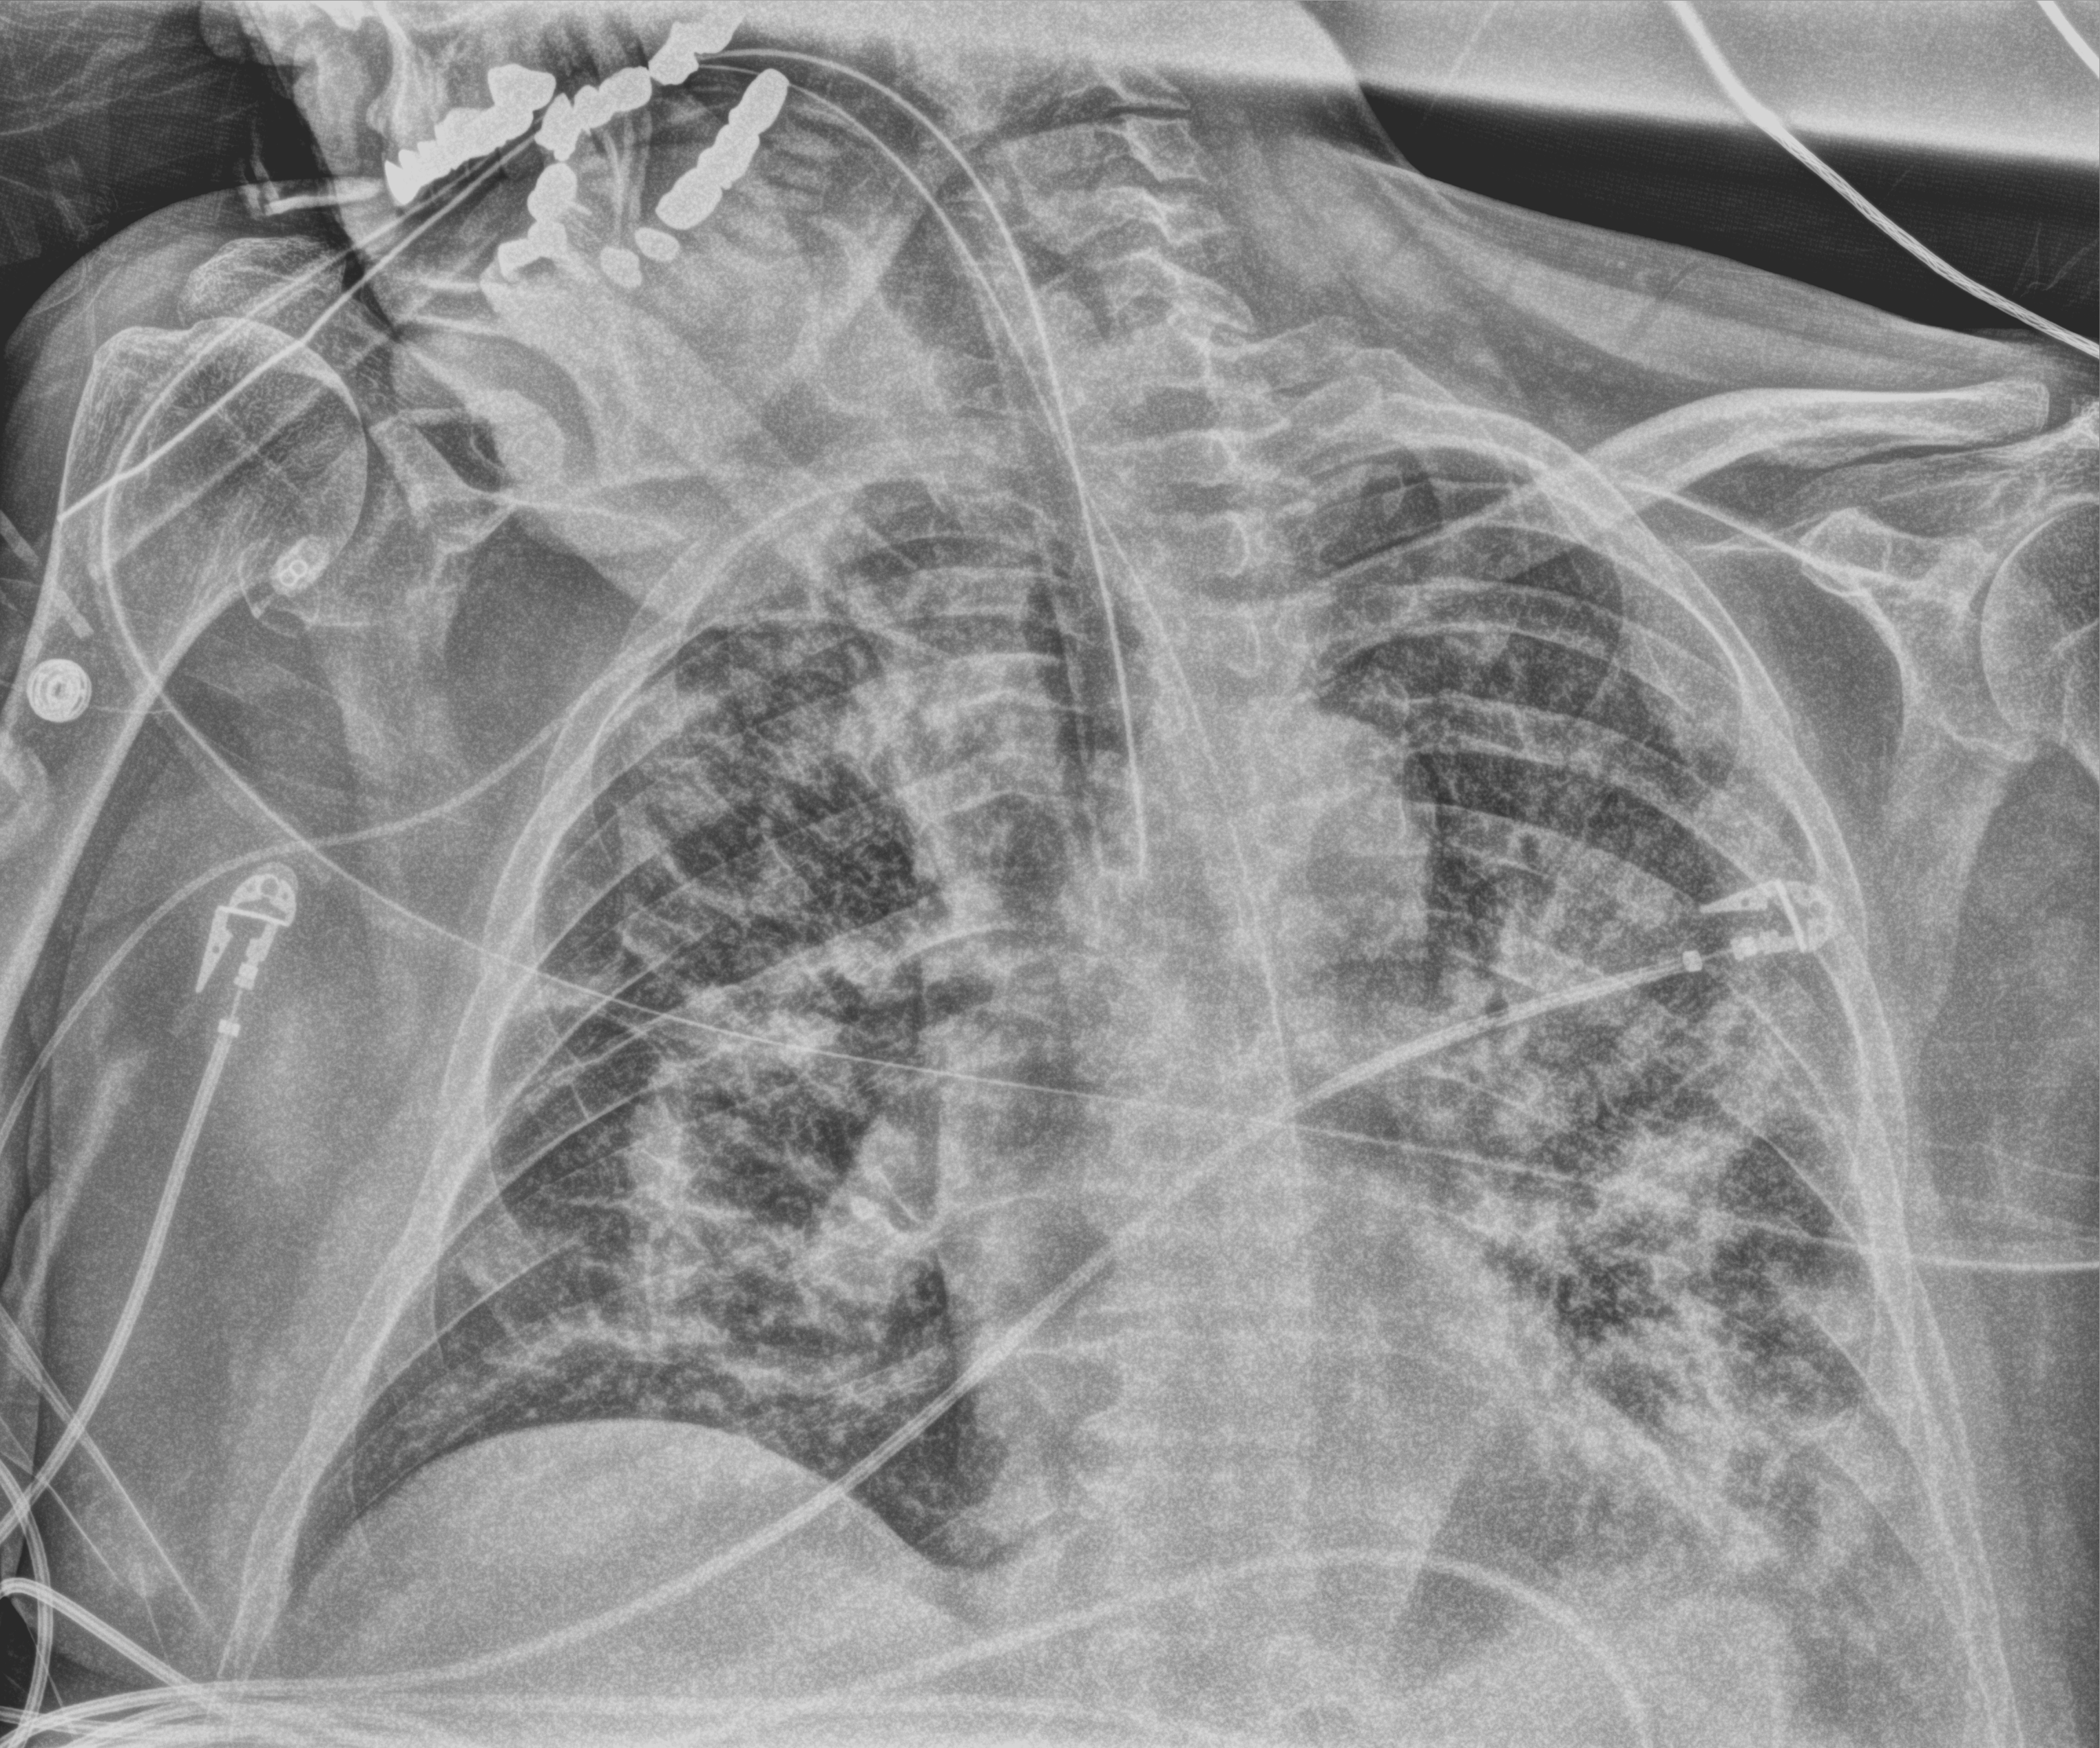
Chest X-ray (portable), anteroposterior (AP) projection. Male patient hospitalised with COVID-19, age 60–74 years.
From the hospital-stay record, not from the radiograph (when in the stay this image was taken is not recorded):
- admitted to intensive care during this hospital stay: yes
- diabetes (admission record): no
- mechanically ventilated during this hospital stay: yes